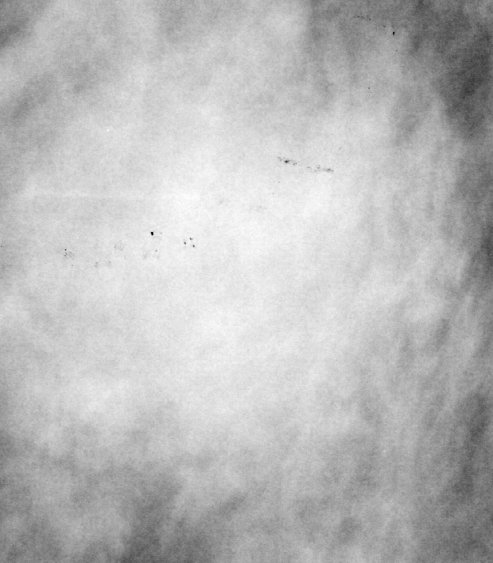
Cropped region of a digitized screen-film mammogram centred on a radiologist-marked abnormality; right breast; MLO view; BI-RADS breast density category 3 (scale 1–4).
Marked abnormality: mass, shape round, margins ill defined; BI-RADS assessment category 4; subtlety rating 3 on a 1 (subtle) to 5 (obvious) scale; pathology result (as recorded, not read from the image): malignant.